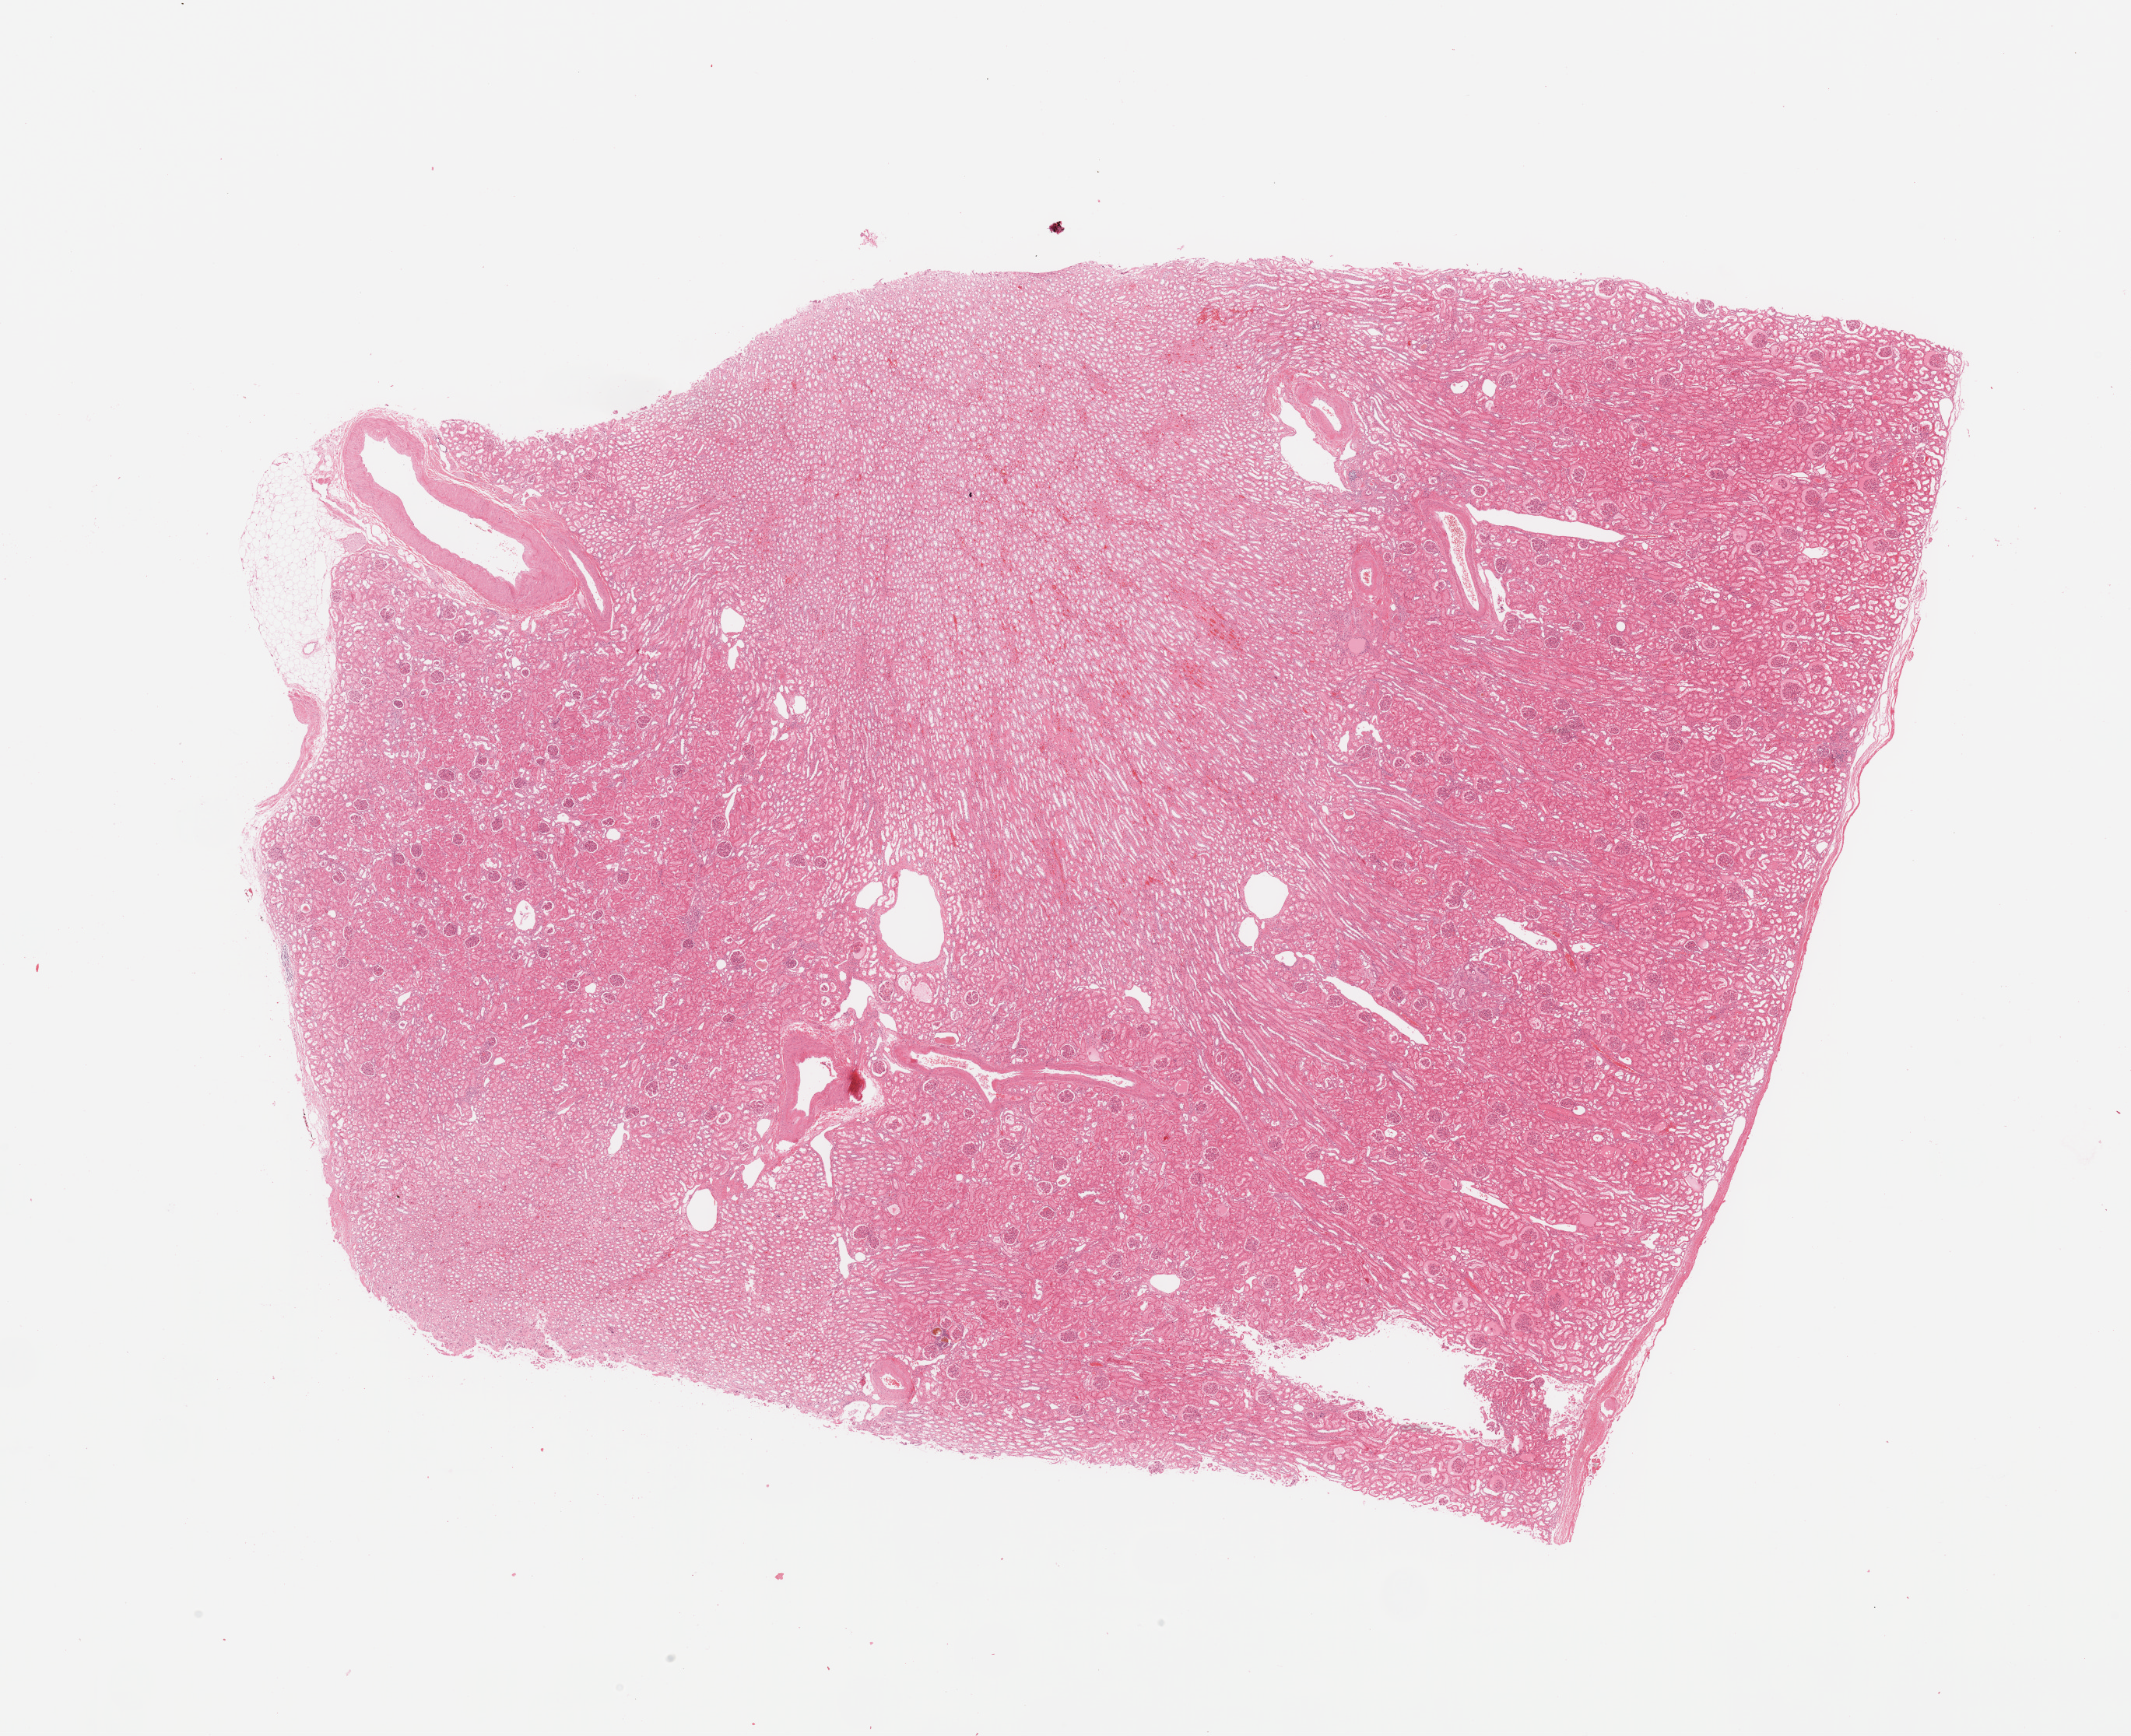
Digitized H&E-stained tissue section (whole slide) — whole scanned area (about 21.7 x 17.6 mm, from a 20x scan) shown as a low-resolution overview, normal (non-tumour) tissue sample, sampled site: kidney. 51-year-old male patient.
• this section: normal (non-tumour) tissue from the same patient
• patient diagnosis: Renal cell carcinoma, NOS